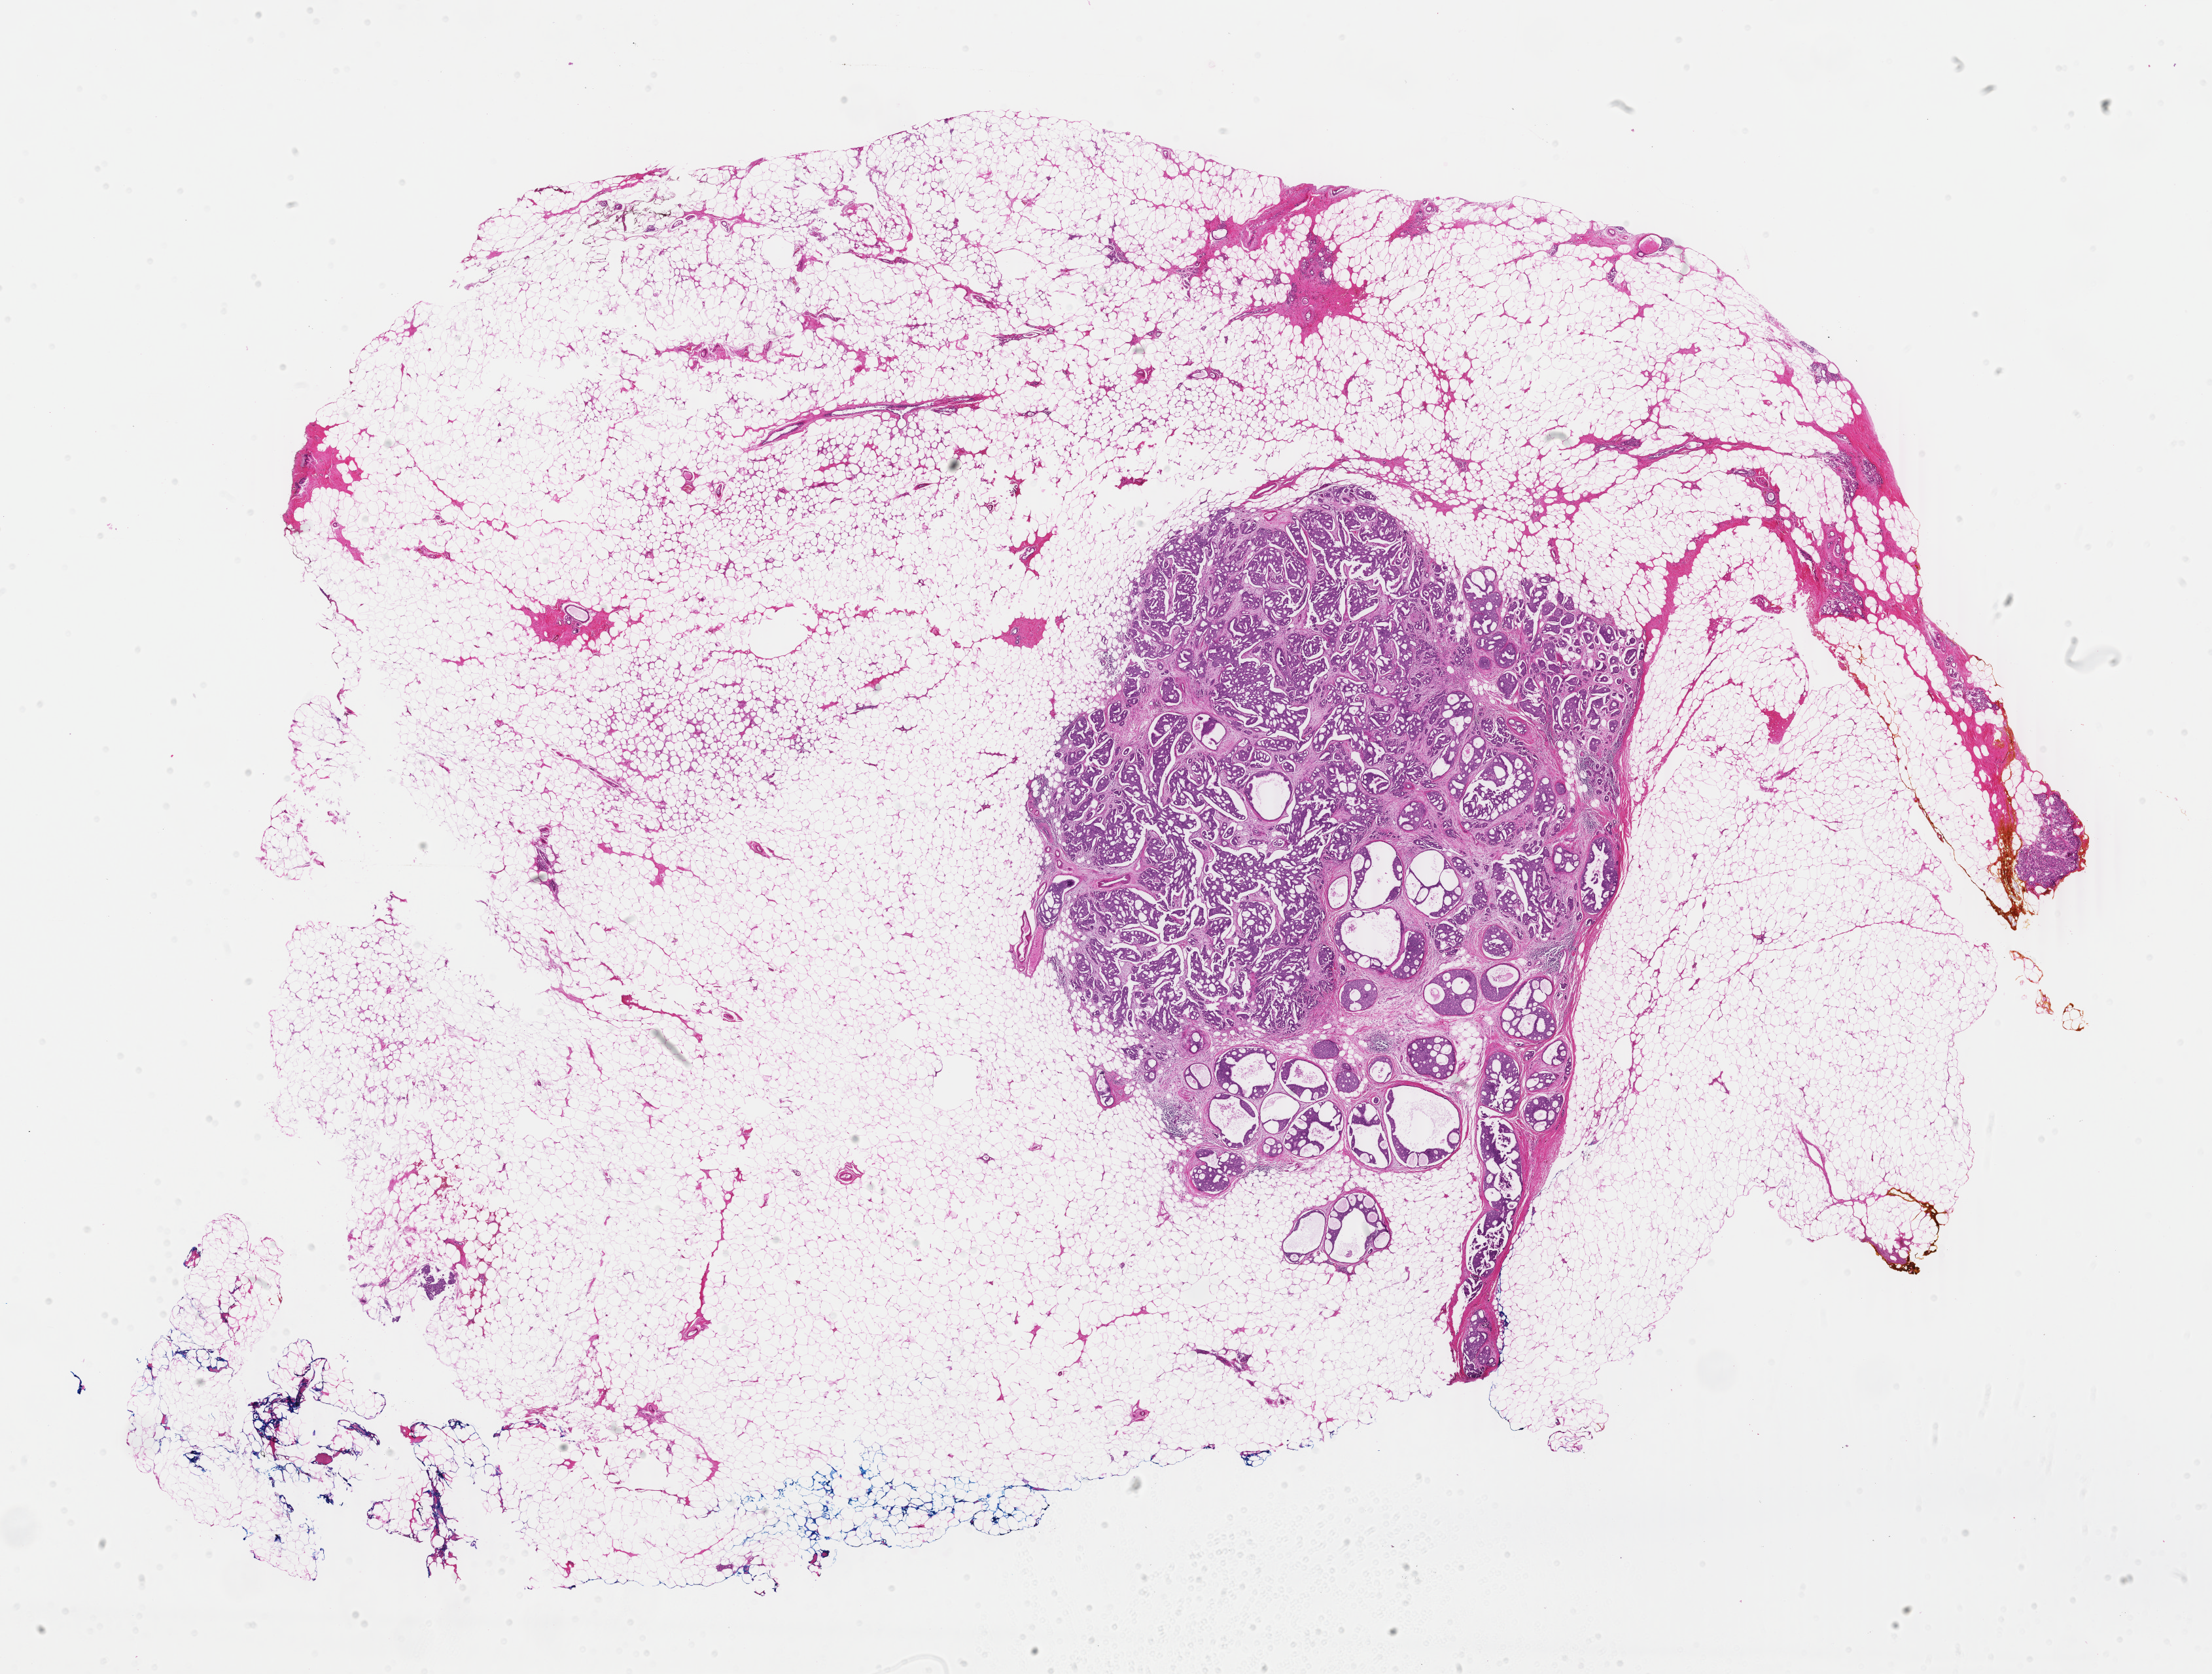
Whole-slide histology image, Hematoxylin and eosin (H&E) stained, low-resolution overview of the scanned area, about 26.9 x 20.4 mm (acquisition: 40x scan); formalin-fixed paraffin-embedded (FFPE) diagnostic section; sample: primary tumour, breast. Female patient; age at initial diagnosis 73 years.
Laterality: right. AJCC pathologic stage: IA. Lymph nodes positive (case pathology): 0 of 1 examined. Diagnosis: Infiltrating duct carcinoma, NOS.